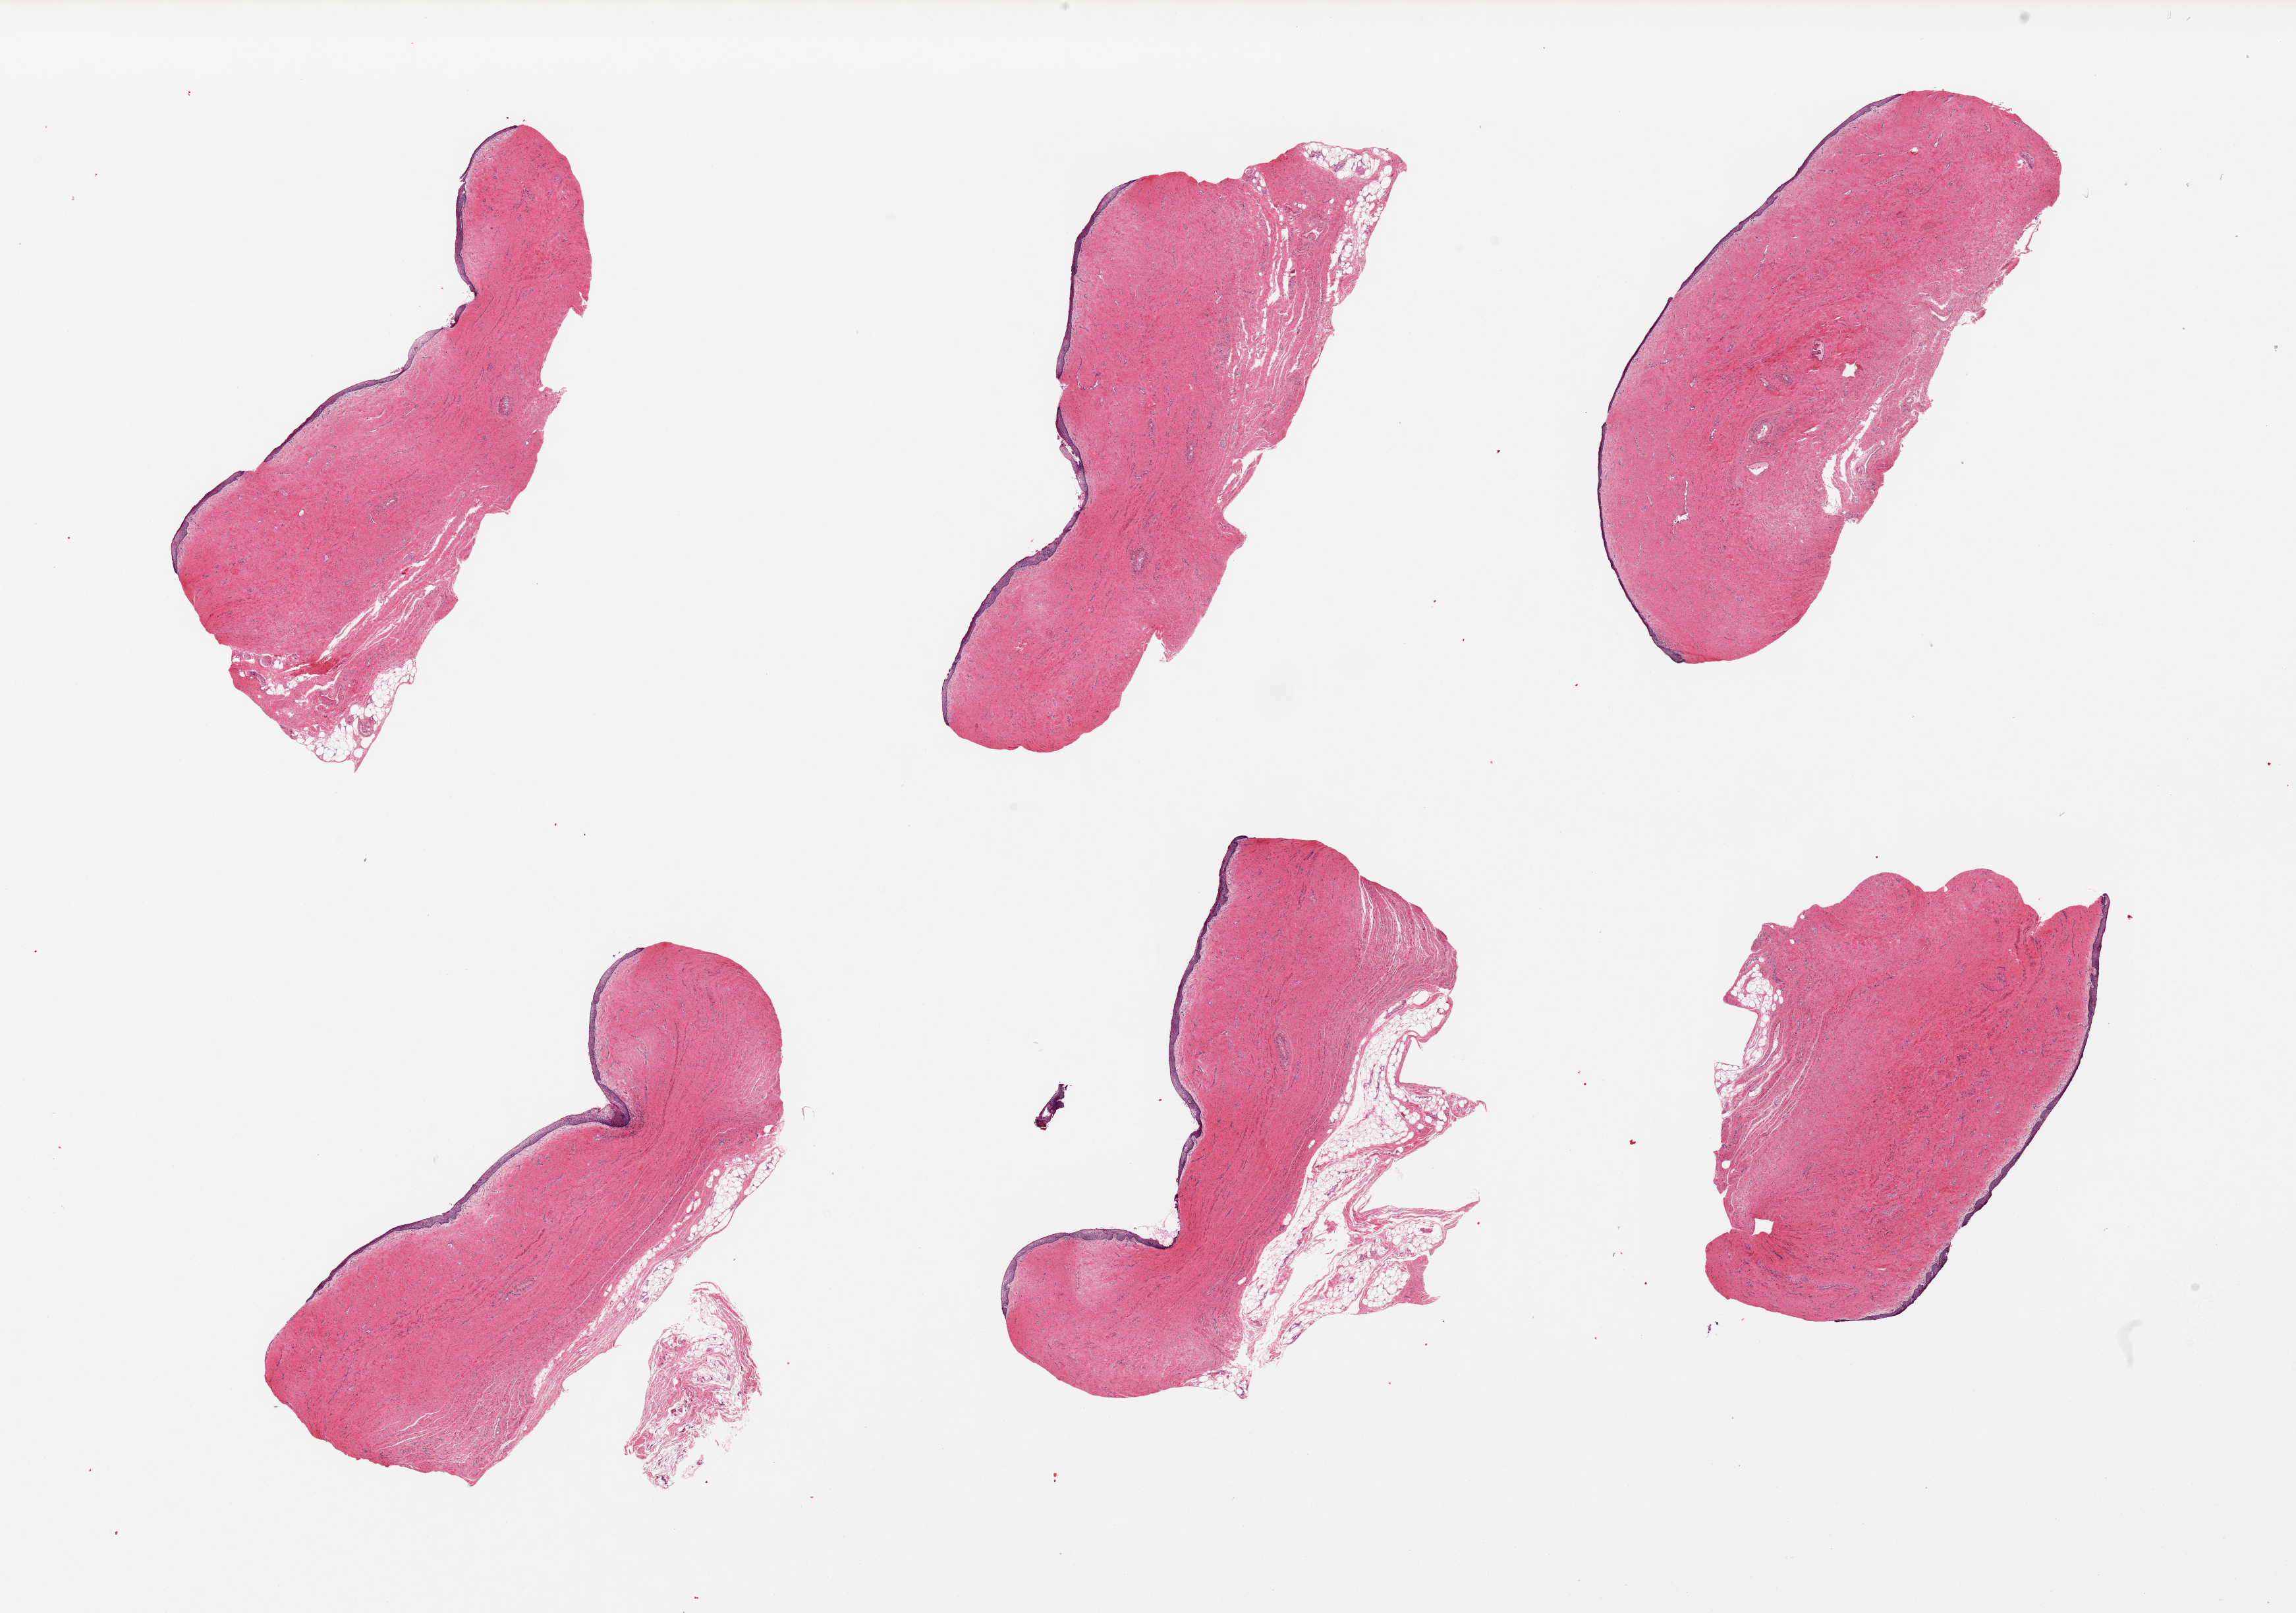
Digitized H&E-stained section, brightfield — a low-resolution overview of the entire scanned area, about 27.6 x 19.4 mm; PAXgene-fixed paraffin-embedded (PFPE) section; target tissue: vagina; tissue donor sample. Female donor.
Review note (as recorded): 6 pieces; squamous mucosa beginning to slough, ~0.1mm thick, 2-3% thickness.